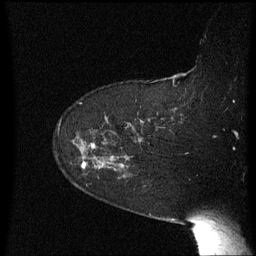
Breast MRI (dynamic contrast-enhanced), one sagittal slice; slice 46 of 60 in the series (ordered by position); dynamic contrast-enhanced series, image 2 of 3 at this slice position (ordered by acquisition); 1.5 T; TE 4.2 ms, TR 8.4 ms; 256 × 256 image matrix, field of view 200 × 200 mm. Patient: female, 63 years. From the clinical record (not read from this slice): setting: breast cancer imaged before/during neoadjuvant chemotherapy; receptor status: HER2-positive.
Outlined on this slice (semi-automatic segmentation, software-assisted and operator-edited):
- analysis volume of interest (the breast-tissue region the enhancement analysis was run in; not a lesion): bounding box <72,136,136,191> (left, top, right, bottom; pixels)
- tumour enhancement mask (voxels above the 70 % enhancement threshold inside the analysis volume of interest): <83,146,93,167>